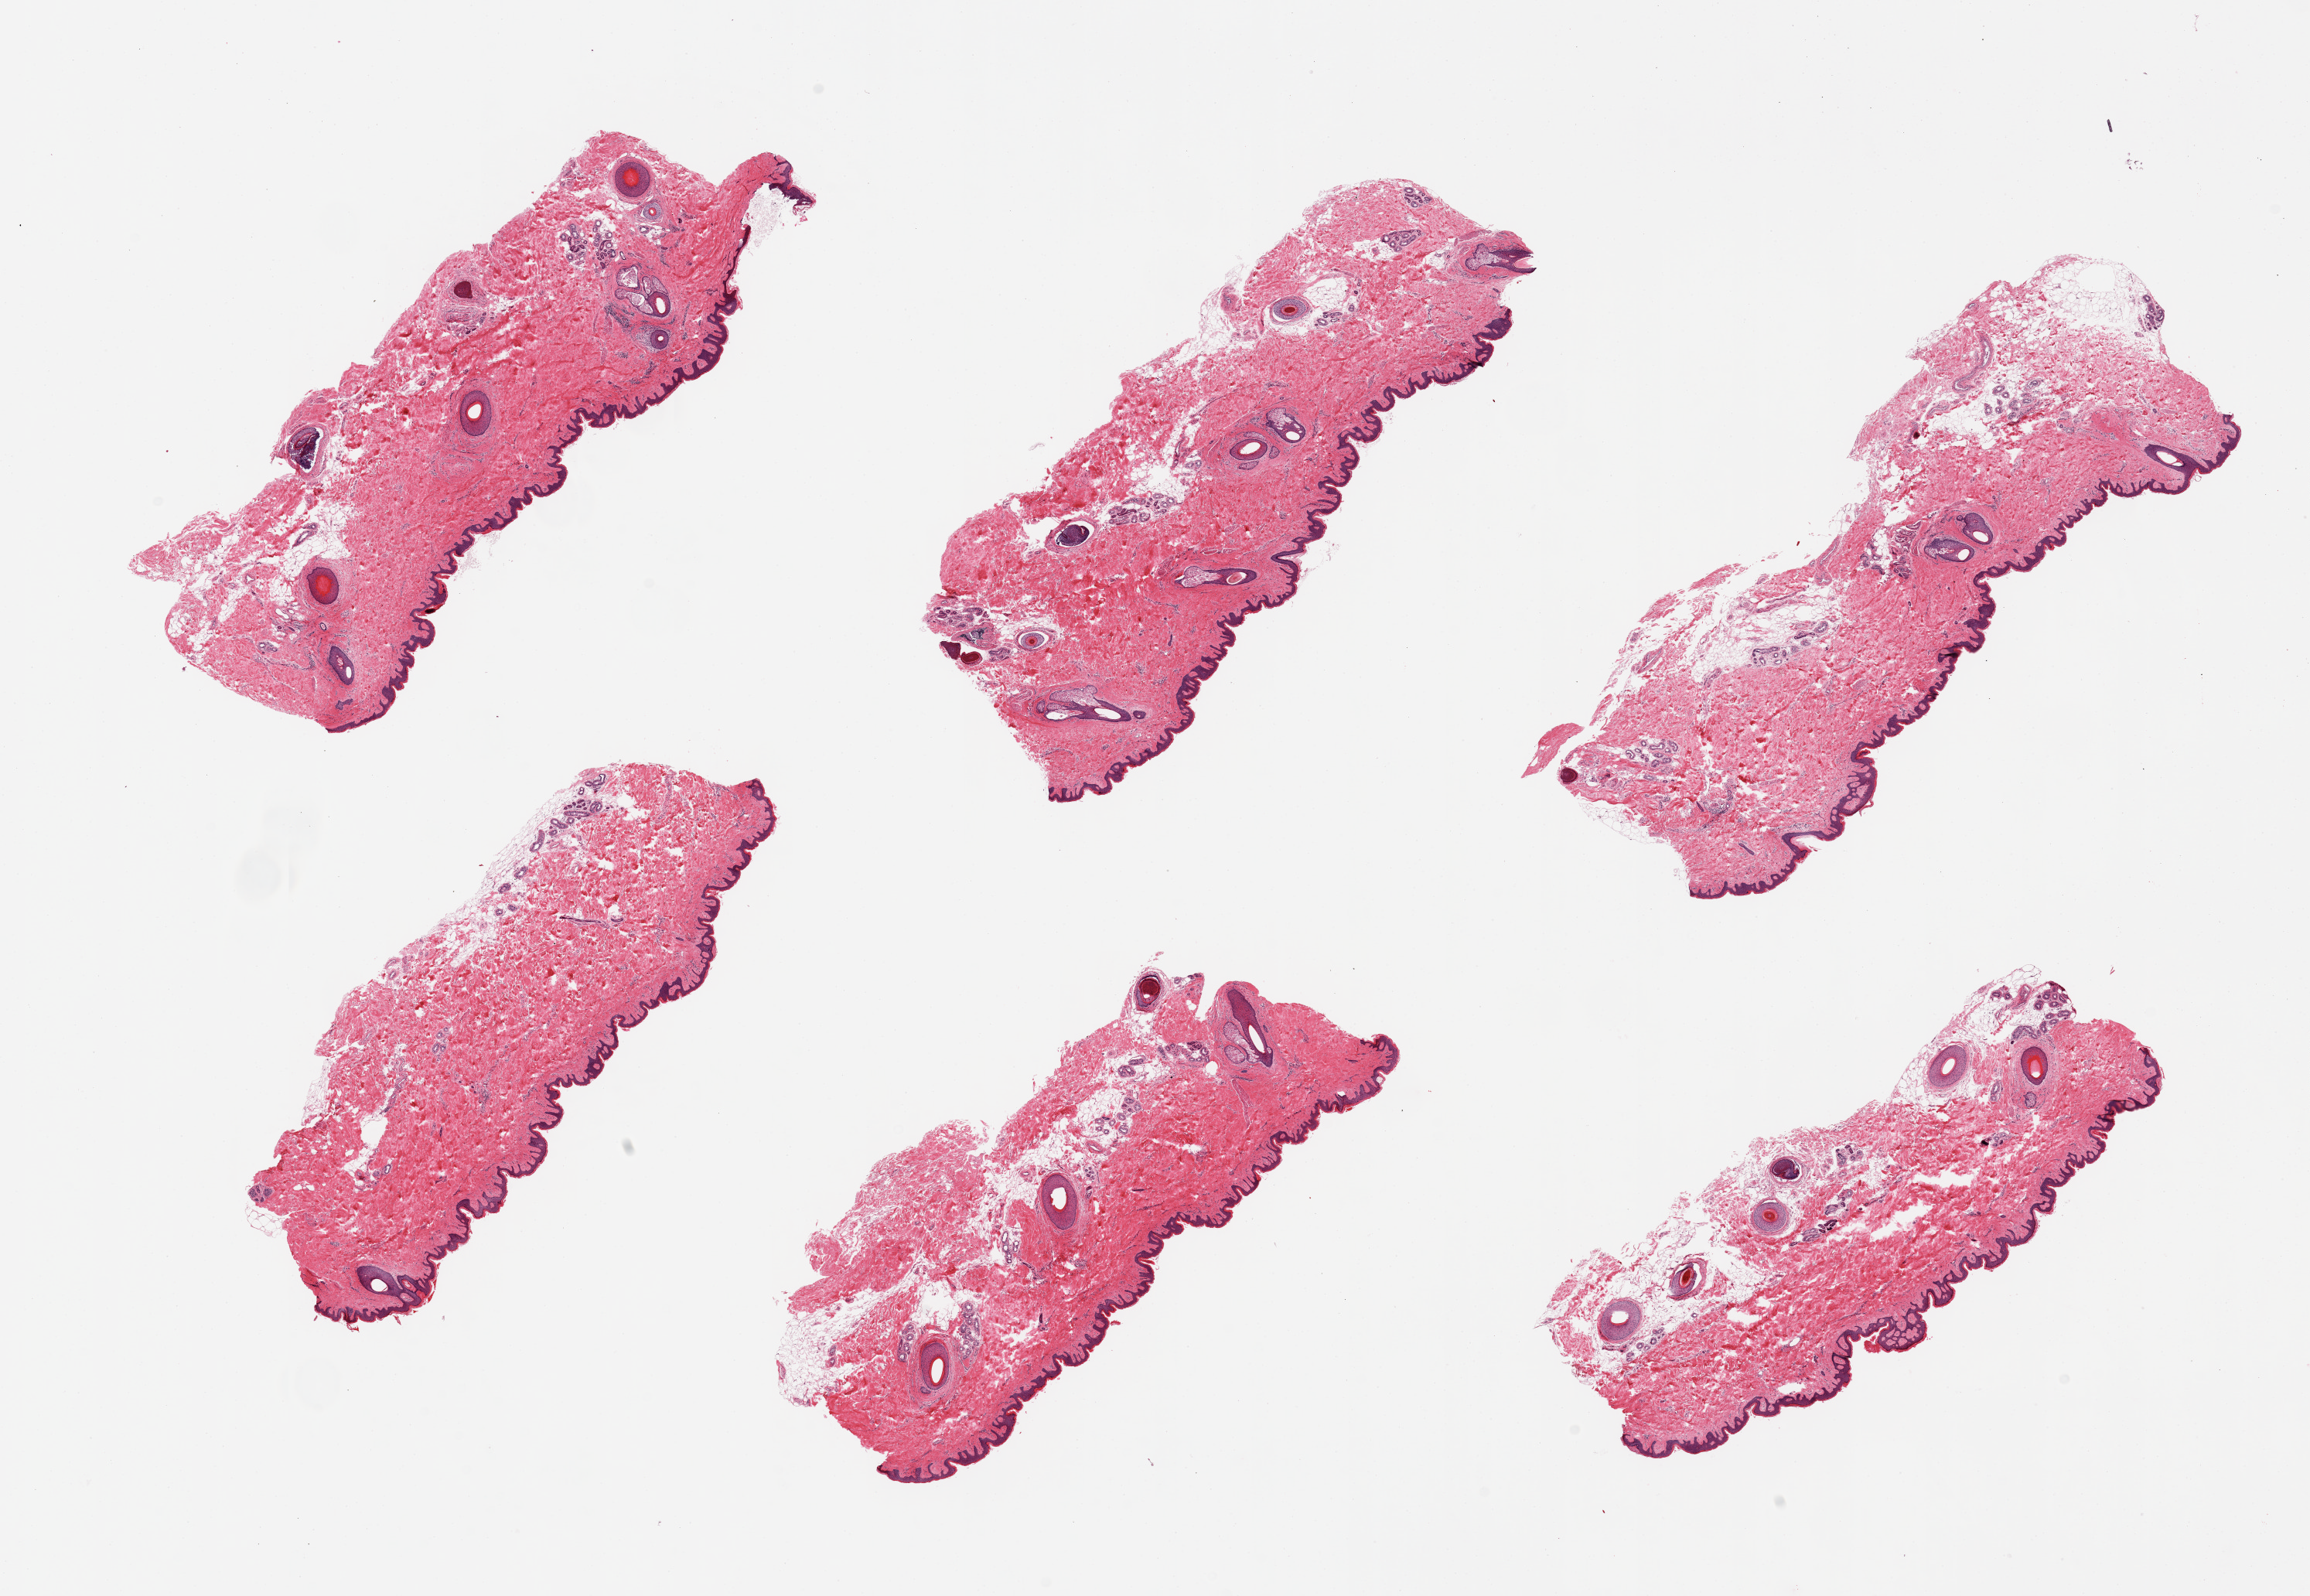
Hematoxylin and eosin (H&E) whole-slide image — shown as a low-resolution overview of the whole scanned area (about 23.6 x 16.3 mm, slide scanned at 20x), PAXgene-fixed, paraffin-embedded tissue, sampled site (target tissue): skin of suprapubic region, tissue donor sample. Donor sex: male.
Review note (as recorded): 6 pieces, 5-20% dermal fat.